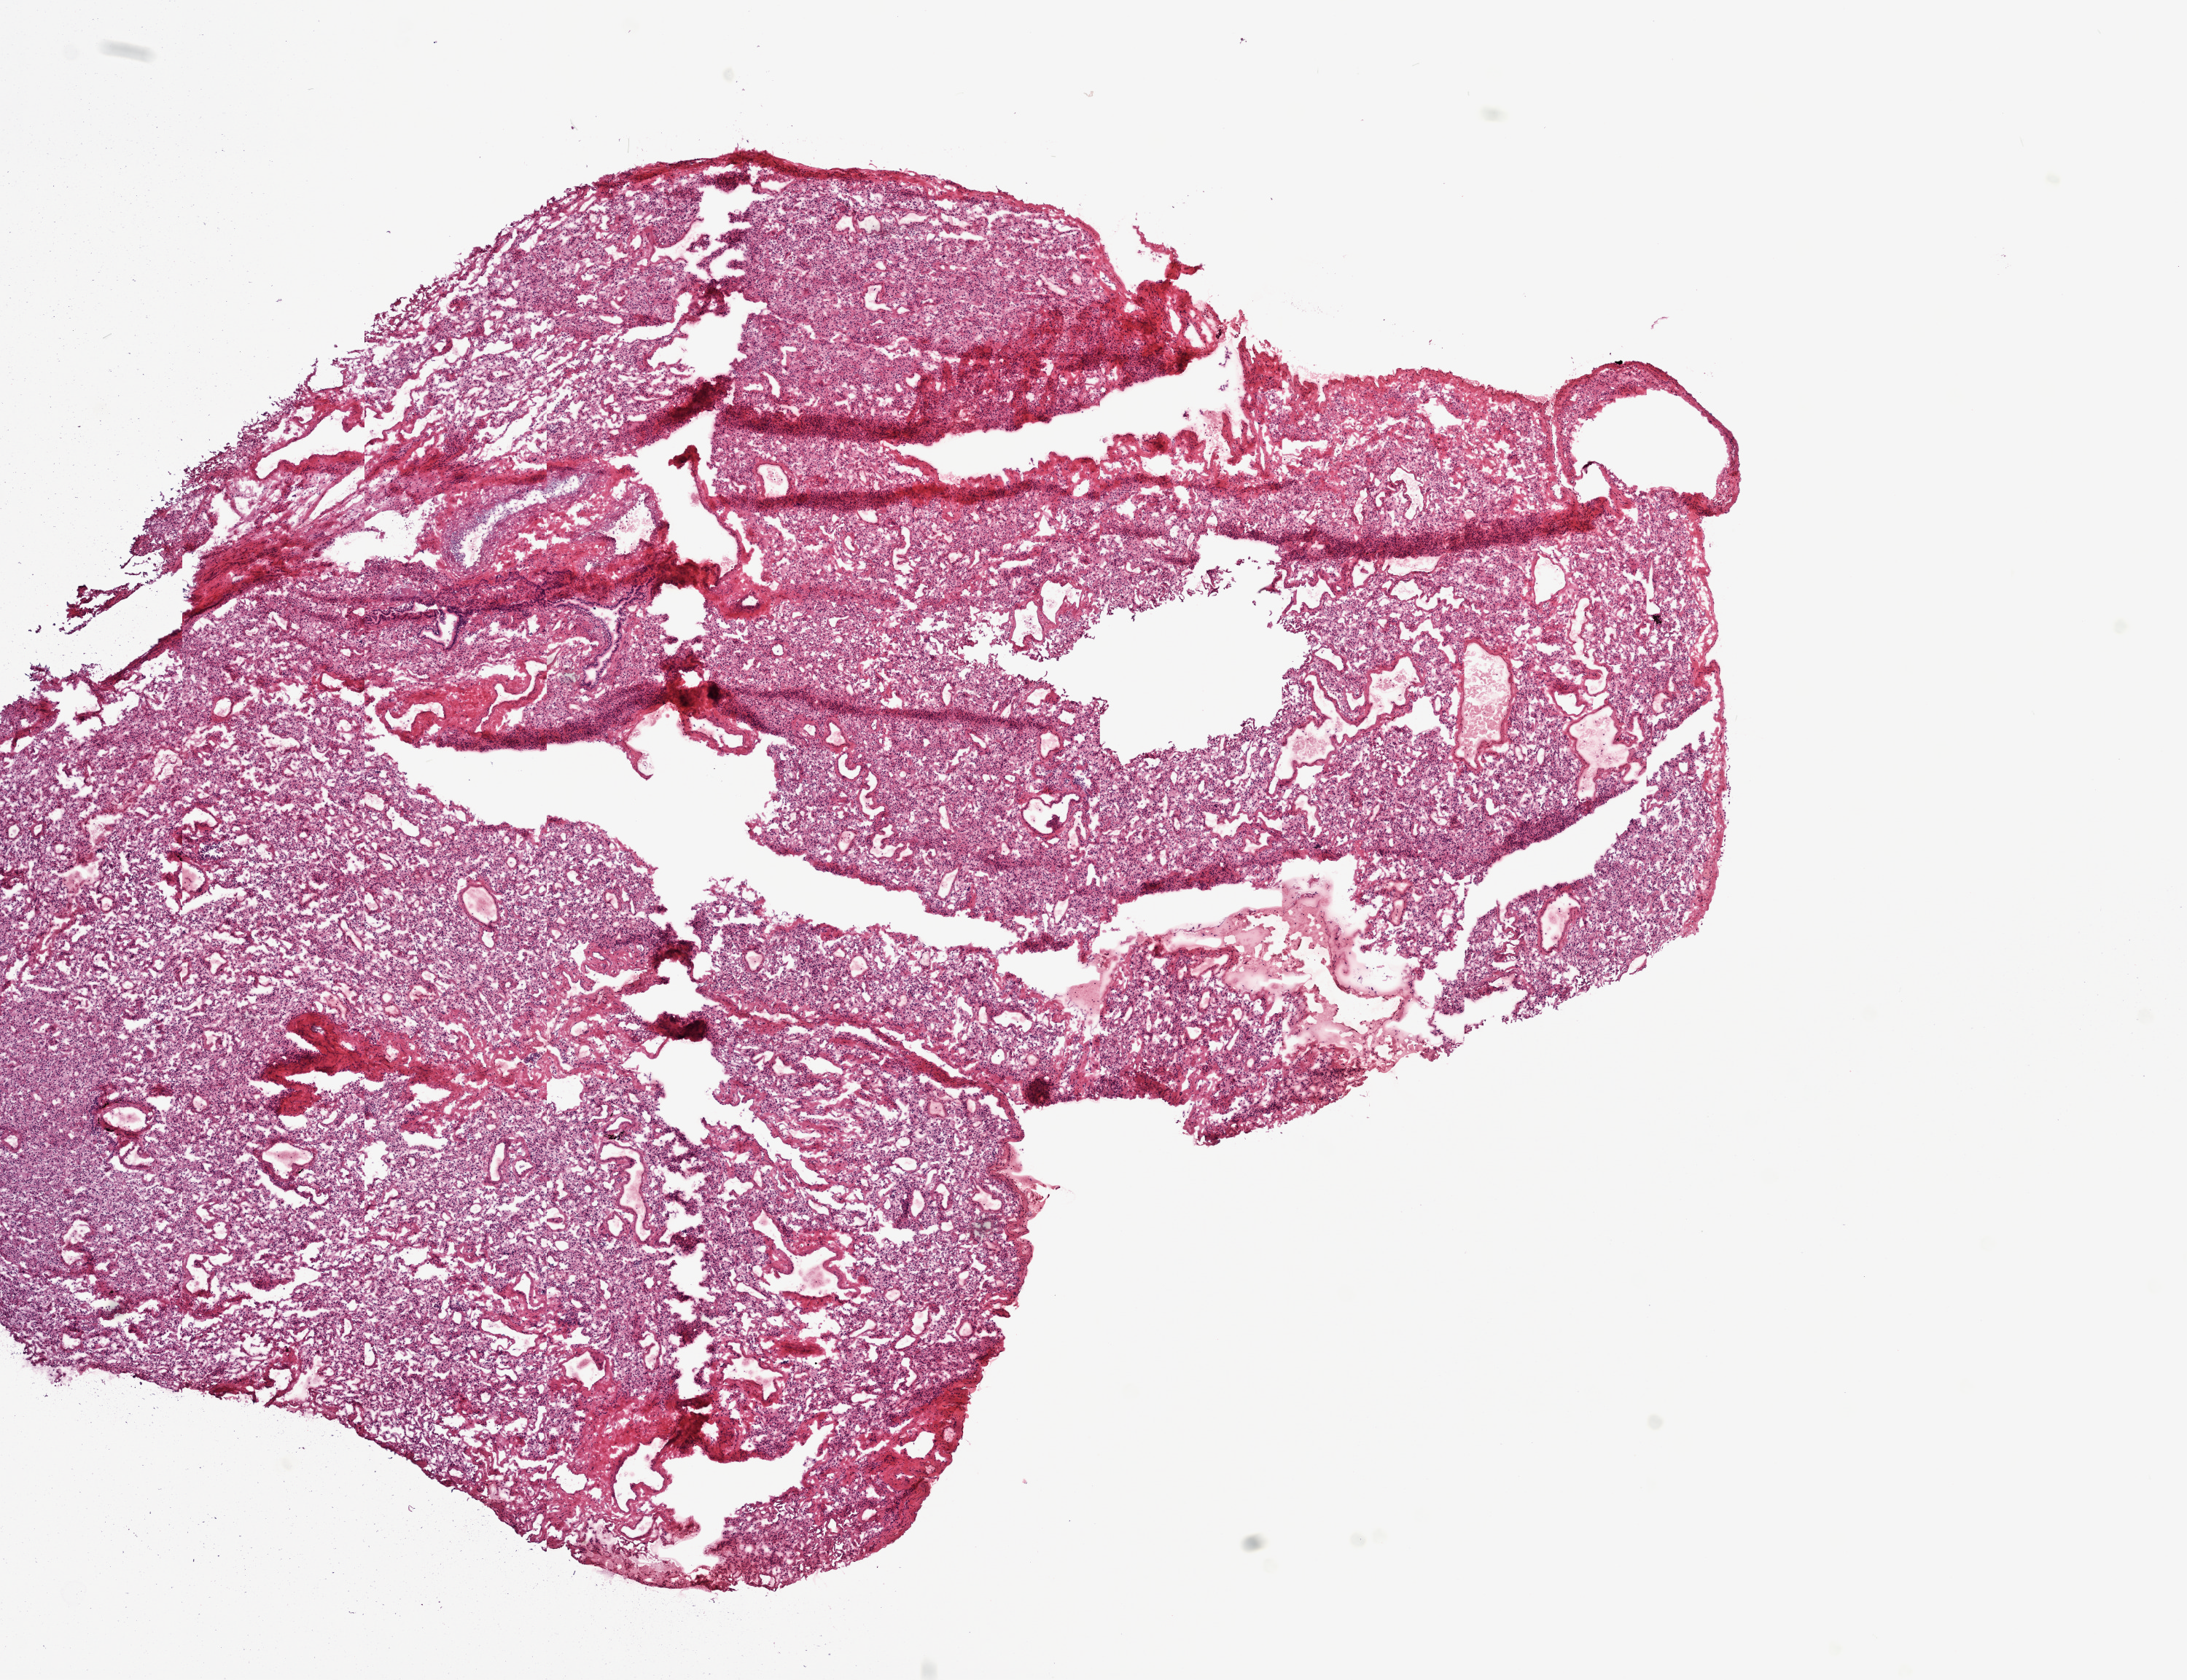
Whole-slide histology image, H&E — a low-resolution overview of the entire scanned area, about 12.0 x 9.2 mm (from a 20x scan), frozen section from the top of the tissue portion, solid tissue normal (non-tumour tissue) sample from the lung. Patient: female, age at initial diagnosis 45 years.
- this section: solid tissue normal (non-tumour) sample from the same patient
- patient diagnosis: Adenocarcinoma, NOS (upper lobe, lung)